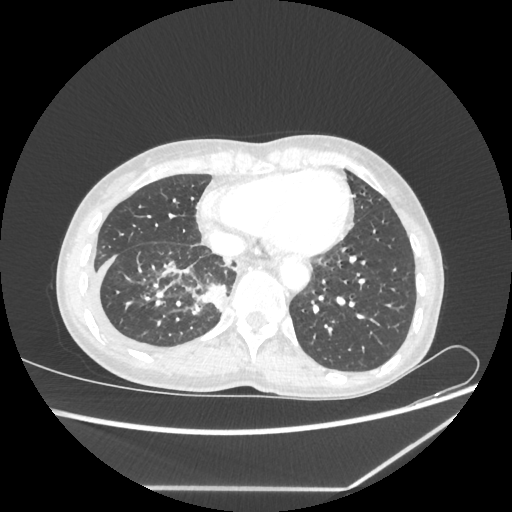
Chest CT, one axial slice. Slice 70 of 237 in the series (ordered by position). Reconstruction kernel STANDARD. 80 kVp. Lung window (W 1500 / L -600 HU). 1.25 mm slice thickness. 512 × 512 image matrix, field of view 364 × 364 mm. Patient: female, 59 years. From the clinical record (not read from this slice): clinical TNM (as recorded): T1c N1 M1.
Structures marked on this image (bounding box drawn by a radiologist):
- lung tumour (recorded histology: adenocarcinoma): bounding box [x1, y1, x2, y2] px = [201, 283, 228, 313]